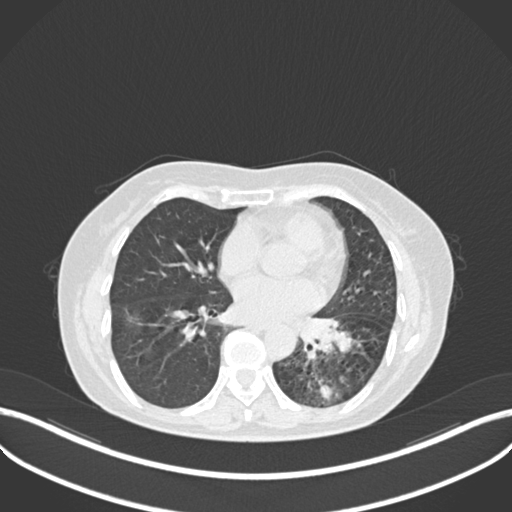
Chest CT, one axial slice; position 114 of 270 along the scan axis; reconstruction kernel B30f; 120 kVp; lung window (W 1500 / L -600 HU); 1 mm slice thickness; 512 × 512 image matrix, field of view 400 × 400 mm. Female patient, age 63 years. Case-level facts recorded for this patient, not image findings: clinical TNM (as recorded): T1b N0 M0; histopathological grade: G2-3.
Annotated regions visible in this slice (bounding box drawn by a radiologist):
- lung tumour (recorded histology: adenocarcinoma): bounding box (x1, y1, x2, y2) in pixels: (292, 310, 354, 356)